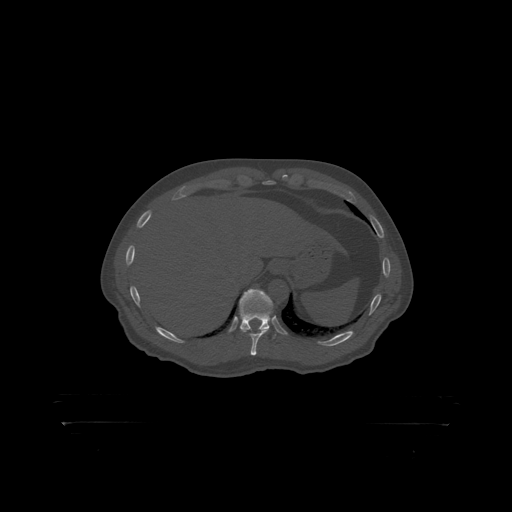
CT including the spine, one axial slice; slice 390 of 399 in the series (ordered by position); bone window (W 1800 / L 400 HU); 512 × 512 image matrix. Patient: male, 46 years. From the clinical record (not read from this slice): primary cancer: skin.
Outlined on this slice (semi-automatic segmentation, software-assisted and operator-edited):
- T11 vertebra: box from (x=240, y=290) to (x=274, y=319) px